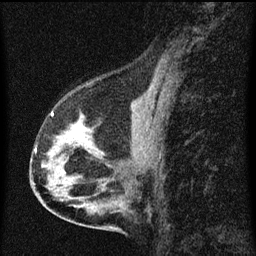
Breast MRI (dynamic contrast-enhanced), one sagittal slice; position 32 of 60 along the scan axis; dynamic contrast-enhanced series, image 2 of 3 at this slice position (ordered by acquisition); 1.5 T; TE 4.2 ms, TR 8 ms; 2 mm slice thickness; 256 × 256 image matrix, field of view 180 × 180 mm. Patient: female, 56 years.
Structures marked on this image (semi-automatic segmentation, software-assisted and operator-edited):
- analysis volume of interest (the breast-tissue region the enhancement analysis was run in; not a lesion): bounding box (x1, y1, x2, y2) in pixels: (34, 114, 102, 181)
- tumour enhancement mask (voxels above the 70 % enhancement threshold inside the analysis volume of interest): (79, 122, 87, 142)